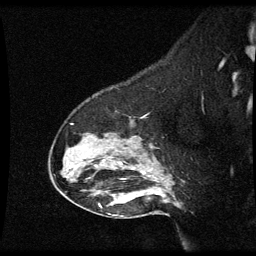
Breast MRI (dynamic contrast-enhanced), one sagittal slice; position 43 of 60 along the scan axis; dynamic contrast-enhanced series, image 2 of 3 at this slice position (ordered by acquisition); 1.5 T; TE 4.2 ms, TR 8.9 ms; 256 × 256 image matrix. Patient: female, 49 years. From the clinical record (not read from this slice): setting: breast cancer imaged before/during neoadjuvant chemotherapy; receptor status: HR-positive, HER2-negative.
Outlined on this slice (semi-automatically segmented with operator editing):
- analysis volume of interest (the breast-tissue region the enhancement analysis was run in; not a lesion): bounding box <50,94,177,205> (left, top, right, bottom; pixels)
- tumour enhancement mask (voxels above the 70 % enhancement threshold inside the analysis volume of interest): <143,172,145,175>